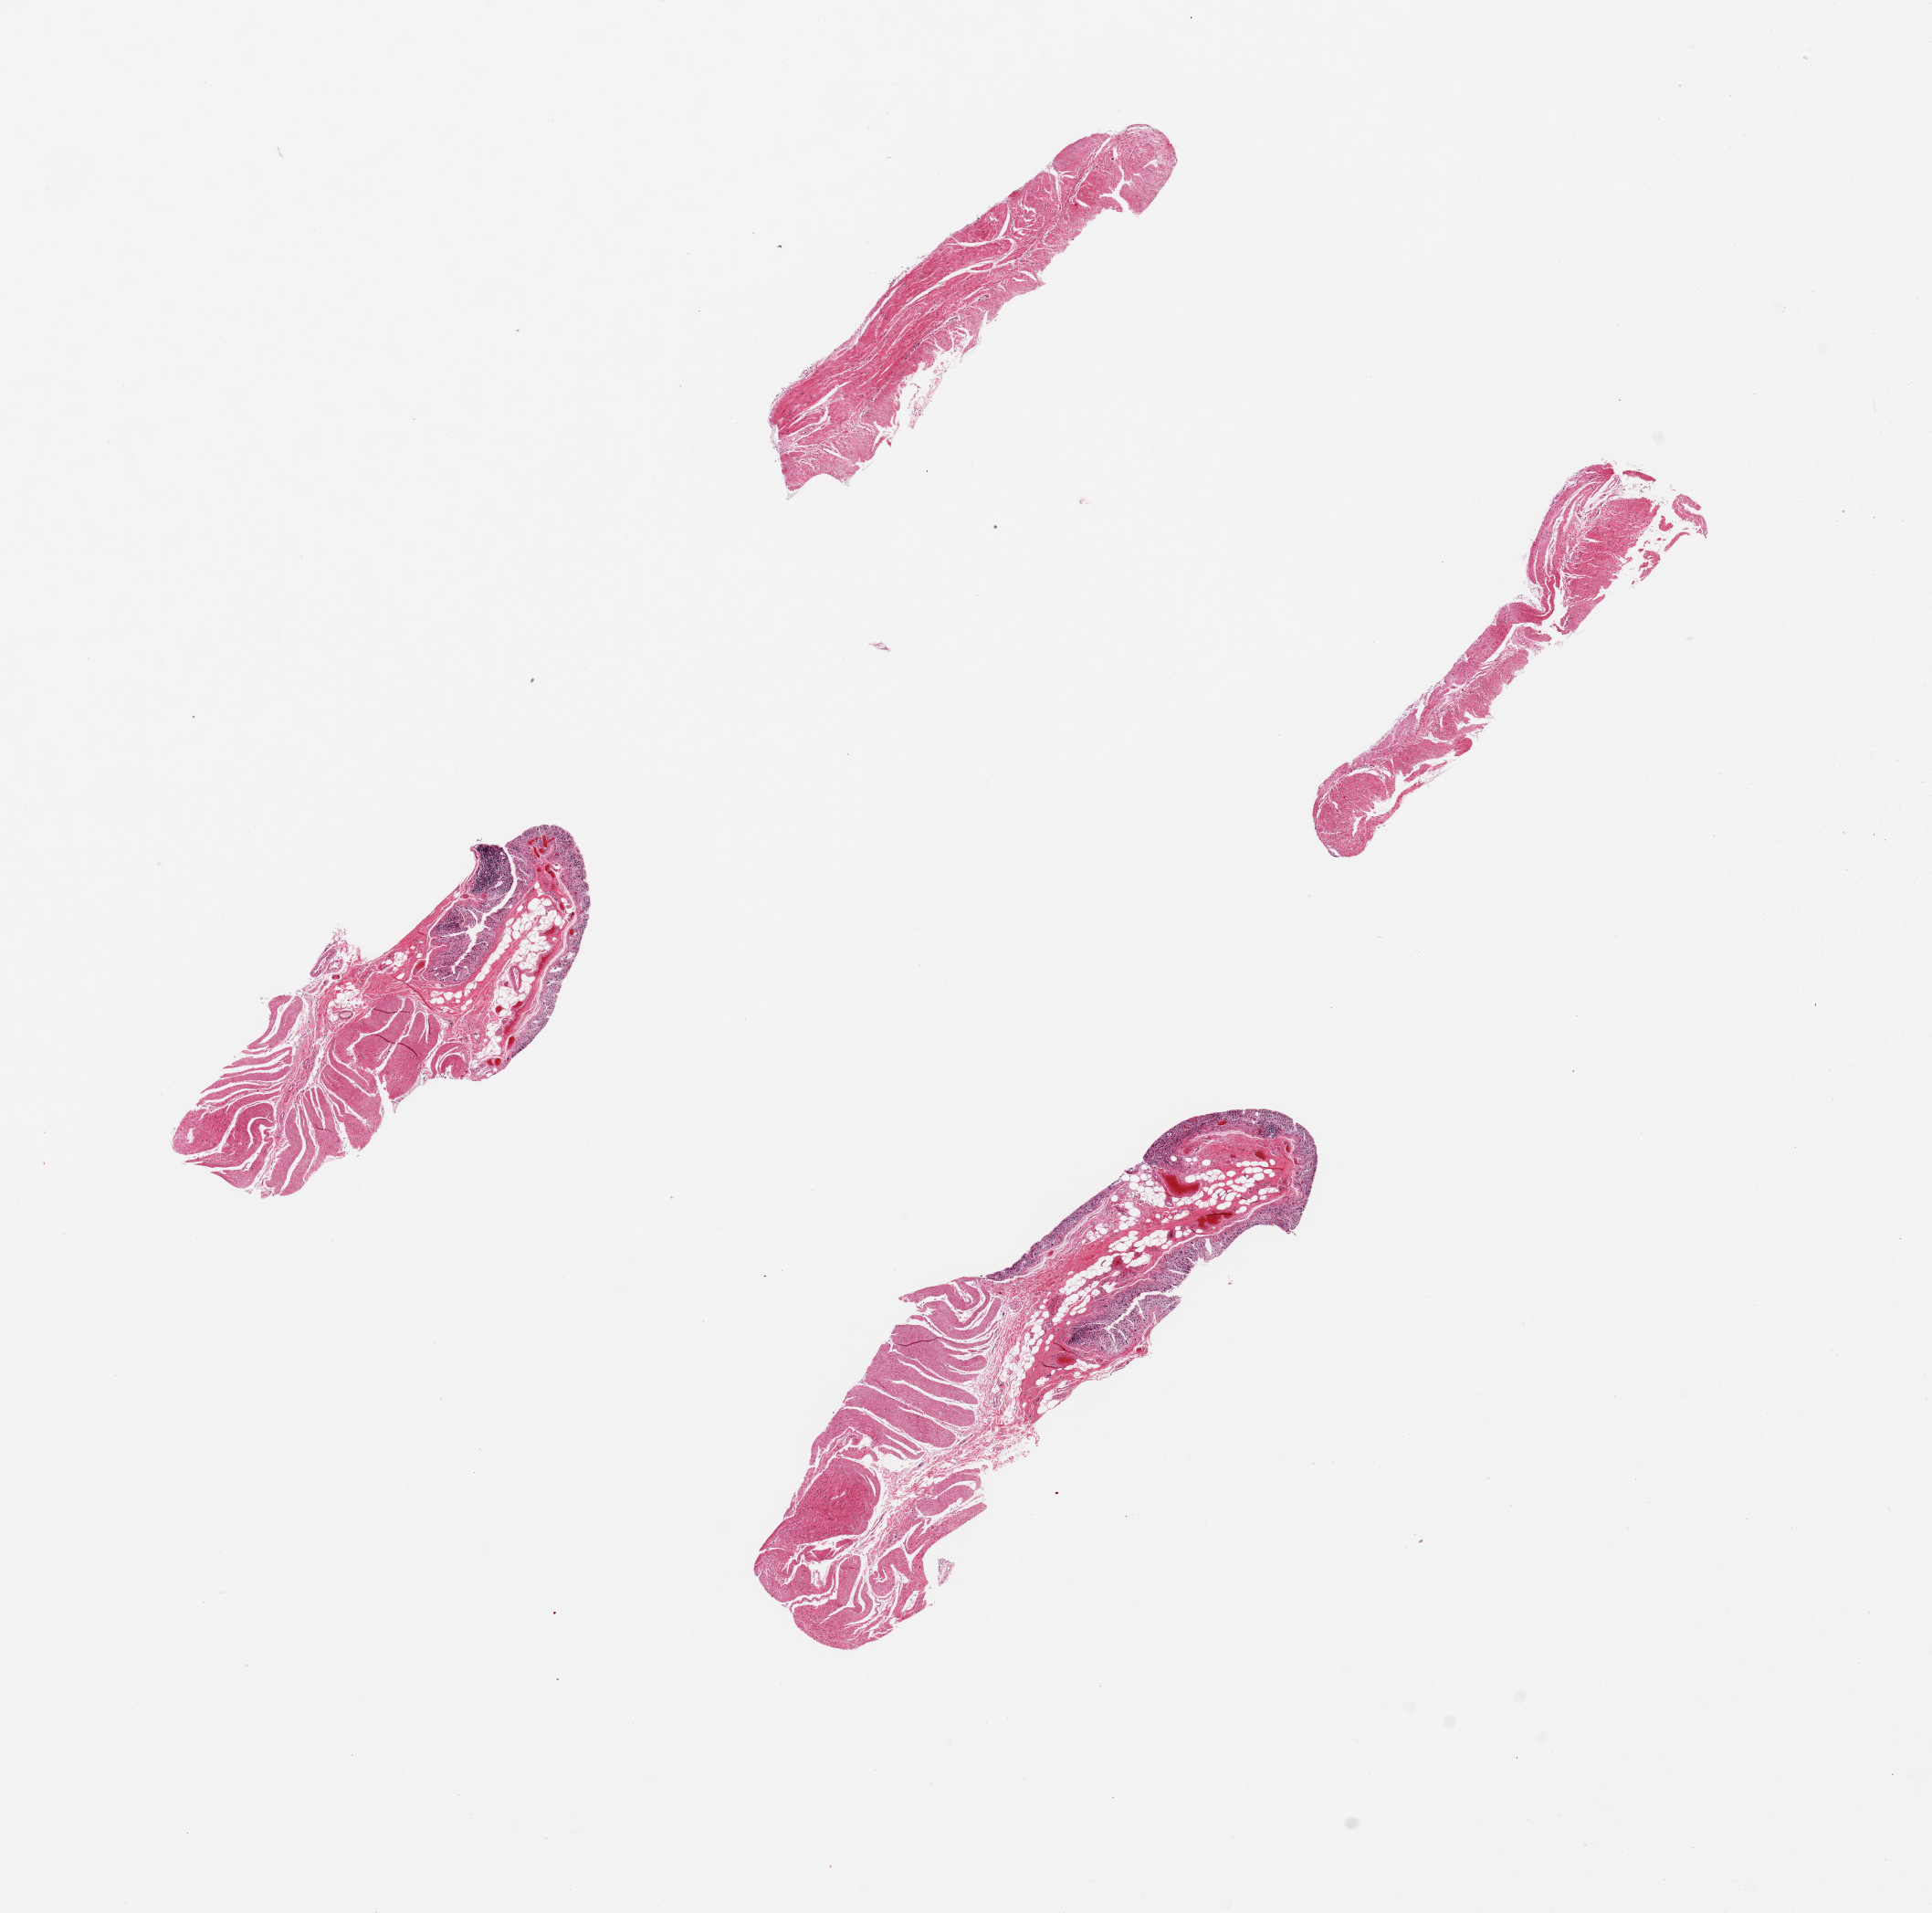
Digitized haematoxylin and eosin-stained section, brightfield — whole scanned area (about 16.7 x 16.6 mm) shown as a low-resolution overview. PAXgene-fixed paraffin-embedded (PFPE) section. Section of sigmoid colon (target tissue). Donor tissue sample.
Pathologist's review note for this sample: 4 pieces, up to 6x2mm; mucosa=3;muscle=2; 2 with mucosa + muscle; 2 with muscle.